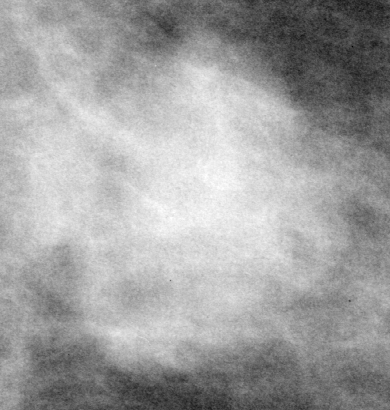
Crop from a digitized film mammogram around one marked abnormality; left breast; MLO view.
Mass, shape oval, margins microlobulated; BI-RADS assessment category 5; subtlety rating 5 on a 1 (subtle) to 5 (obvious) scale; pathology (as recorded): malignant.